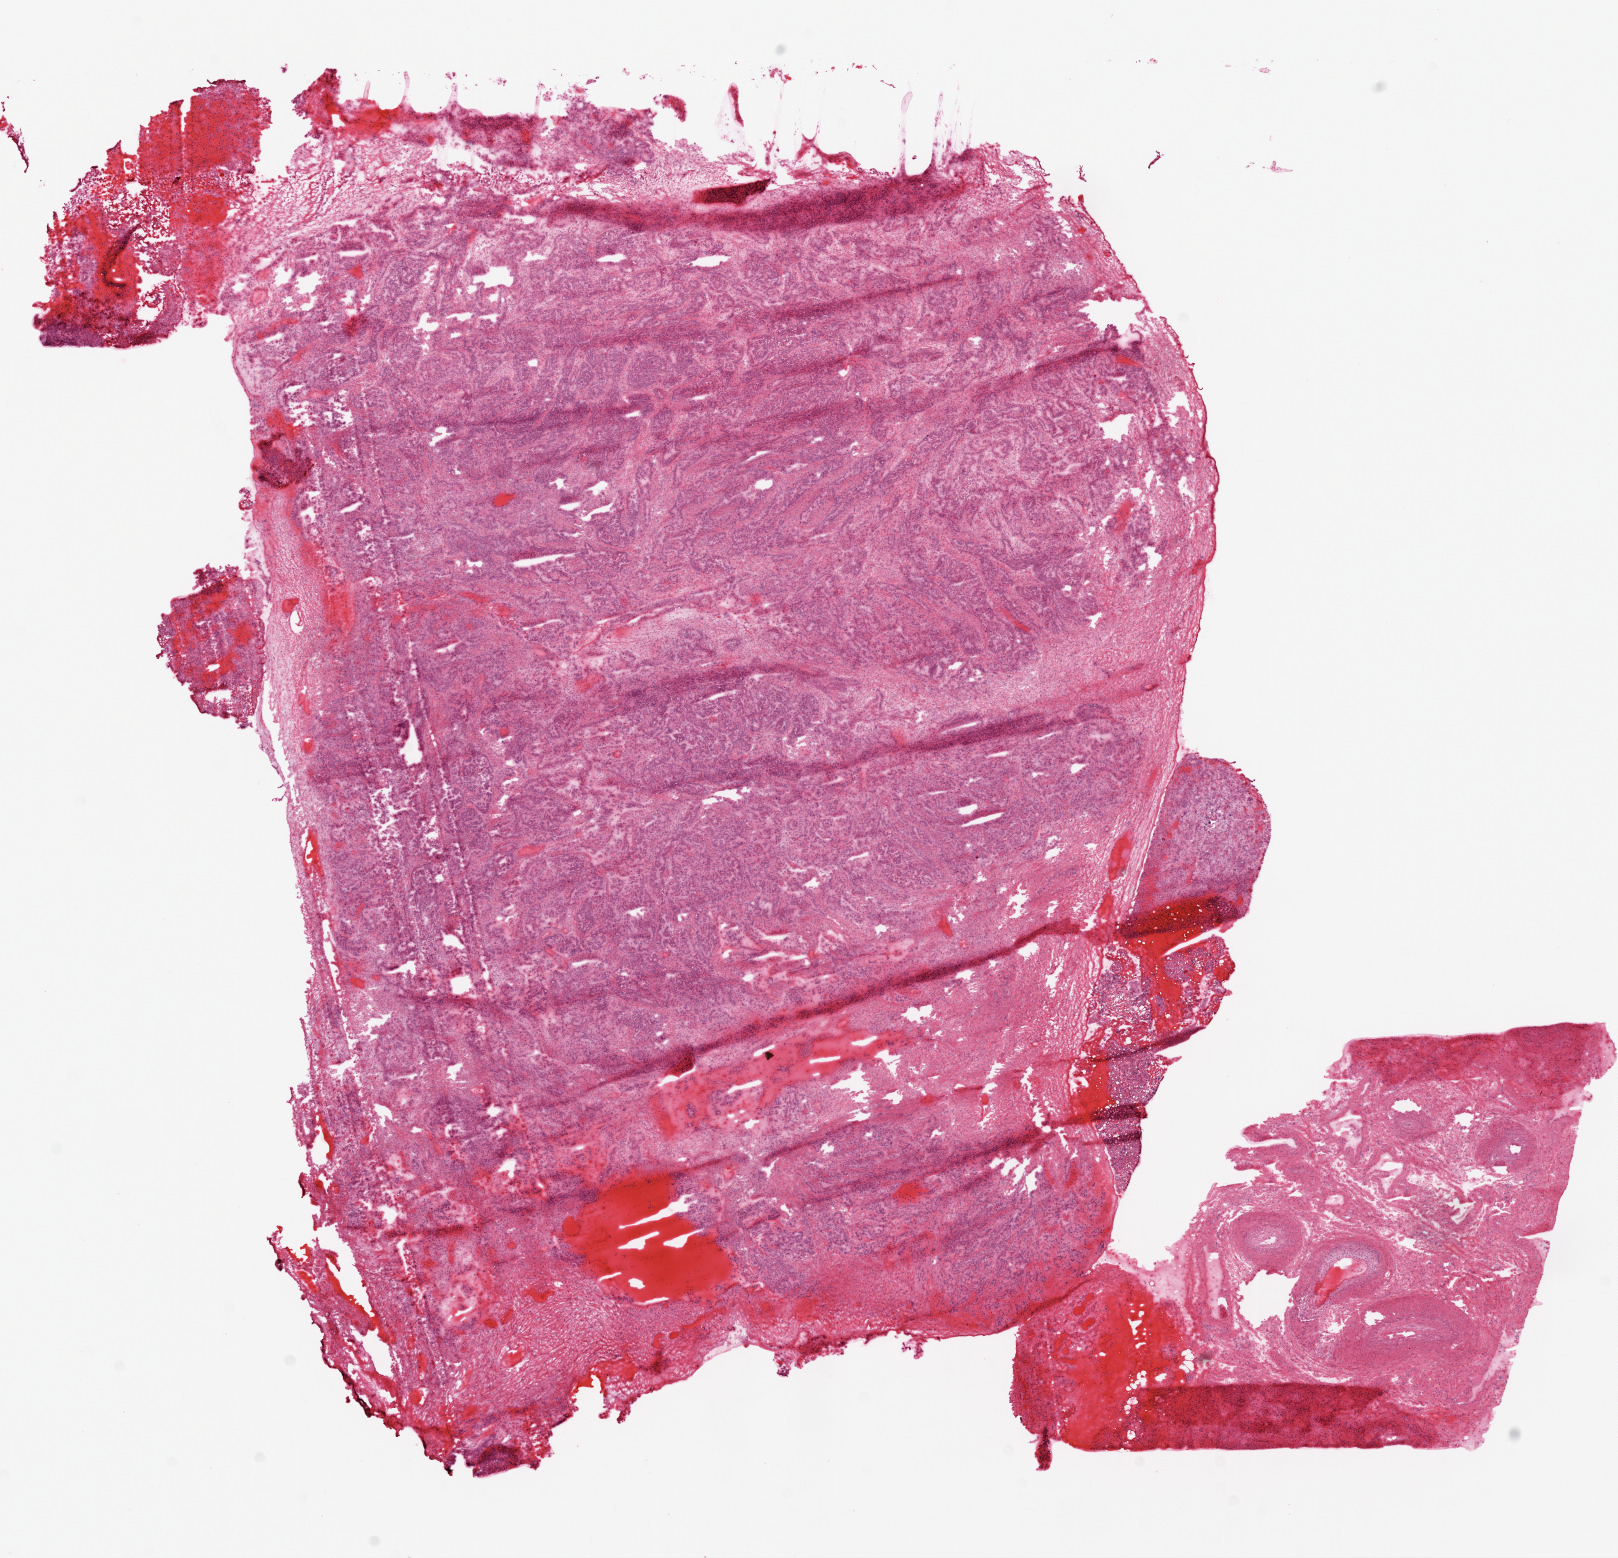
Digitized H&E tissue section (whole slide) — shown as a low-resolution overview of the whole scanned area (about 13.1 x 12.6 mm), frozen section from the top of the tissue portion, ovary, primary tumour sample. Female patient; age at initial diagnosis 62 years. Histologic grade: G3 (poorly differentiated). Composition of this section per pathologist review: tumour cells 70%, tumour nuclei 90%, normal cells 0%, stromal cells 30%, necrosis 0%.
Laterality: bilateral. FIGO stage: IV. Diagnosis: Serous cystadenocarcinoma, NOS.